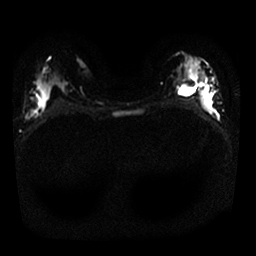
Breast MRI, one axial slice. Position 12 of 25 along the scan axis. Diffusion-weighted series; image 2 of 4 stored at this slice position (different b-values; order by instance number). 1.5 T. 4 mm slice thickness. 256 × 256 image matrix, field of view 320 × 320 mm. Female patient.
Annotated regions visible in this slice (outlined manually by an expert reader):
- tumour on diffusion-weighted imaging: bounding box (x1, y1, x2, y2) in pixels: (202, 87, 212, 107)